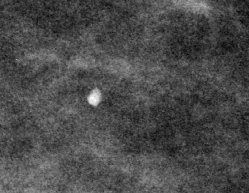
Cropped region of a digitized screen-film mammogram centred on a radiologist-marked abnormality, left breast, MLO view, BI-RADS breast density category 2 (scale 1–4).
Finding: calcifications, morphology punctate; BI-RADS assessment category 2; benign without callback (not worked up further).